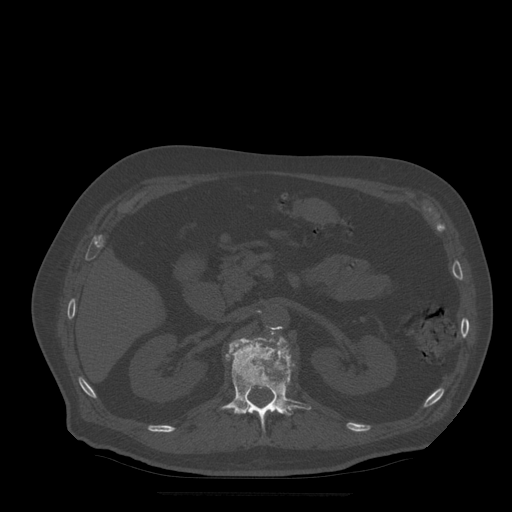
CT including the spine, one axial slice. Slice 196 of 522 in the series (ordered by position). Bone window (W 1800 / L 400 HU). 1.25 mm slice thickness. 512 × 512 image matrix, field of view 420 × 420 mm. Patient age 72 years. Case-level facts recorded for this patient, not image findings: primary cancer: prostate.
Outlined on this slice (semi-automatically segmented with operator editing):
- L1 vertebra: bounding box <221,337,312,431> (left, top, right, bottom; pixels)
- L2 vertebra: <271,331,275,335>